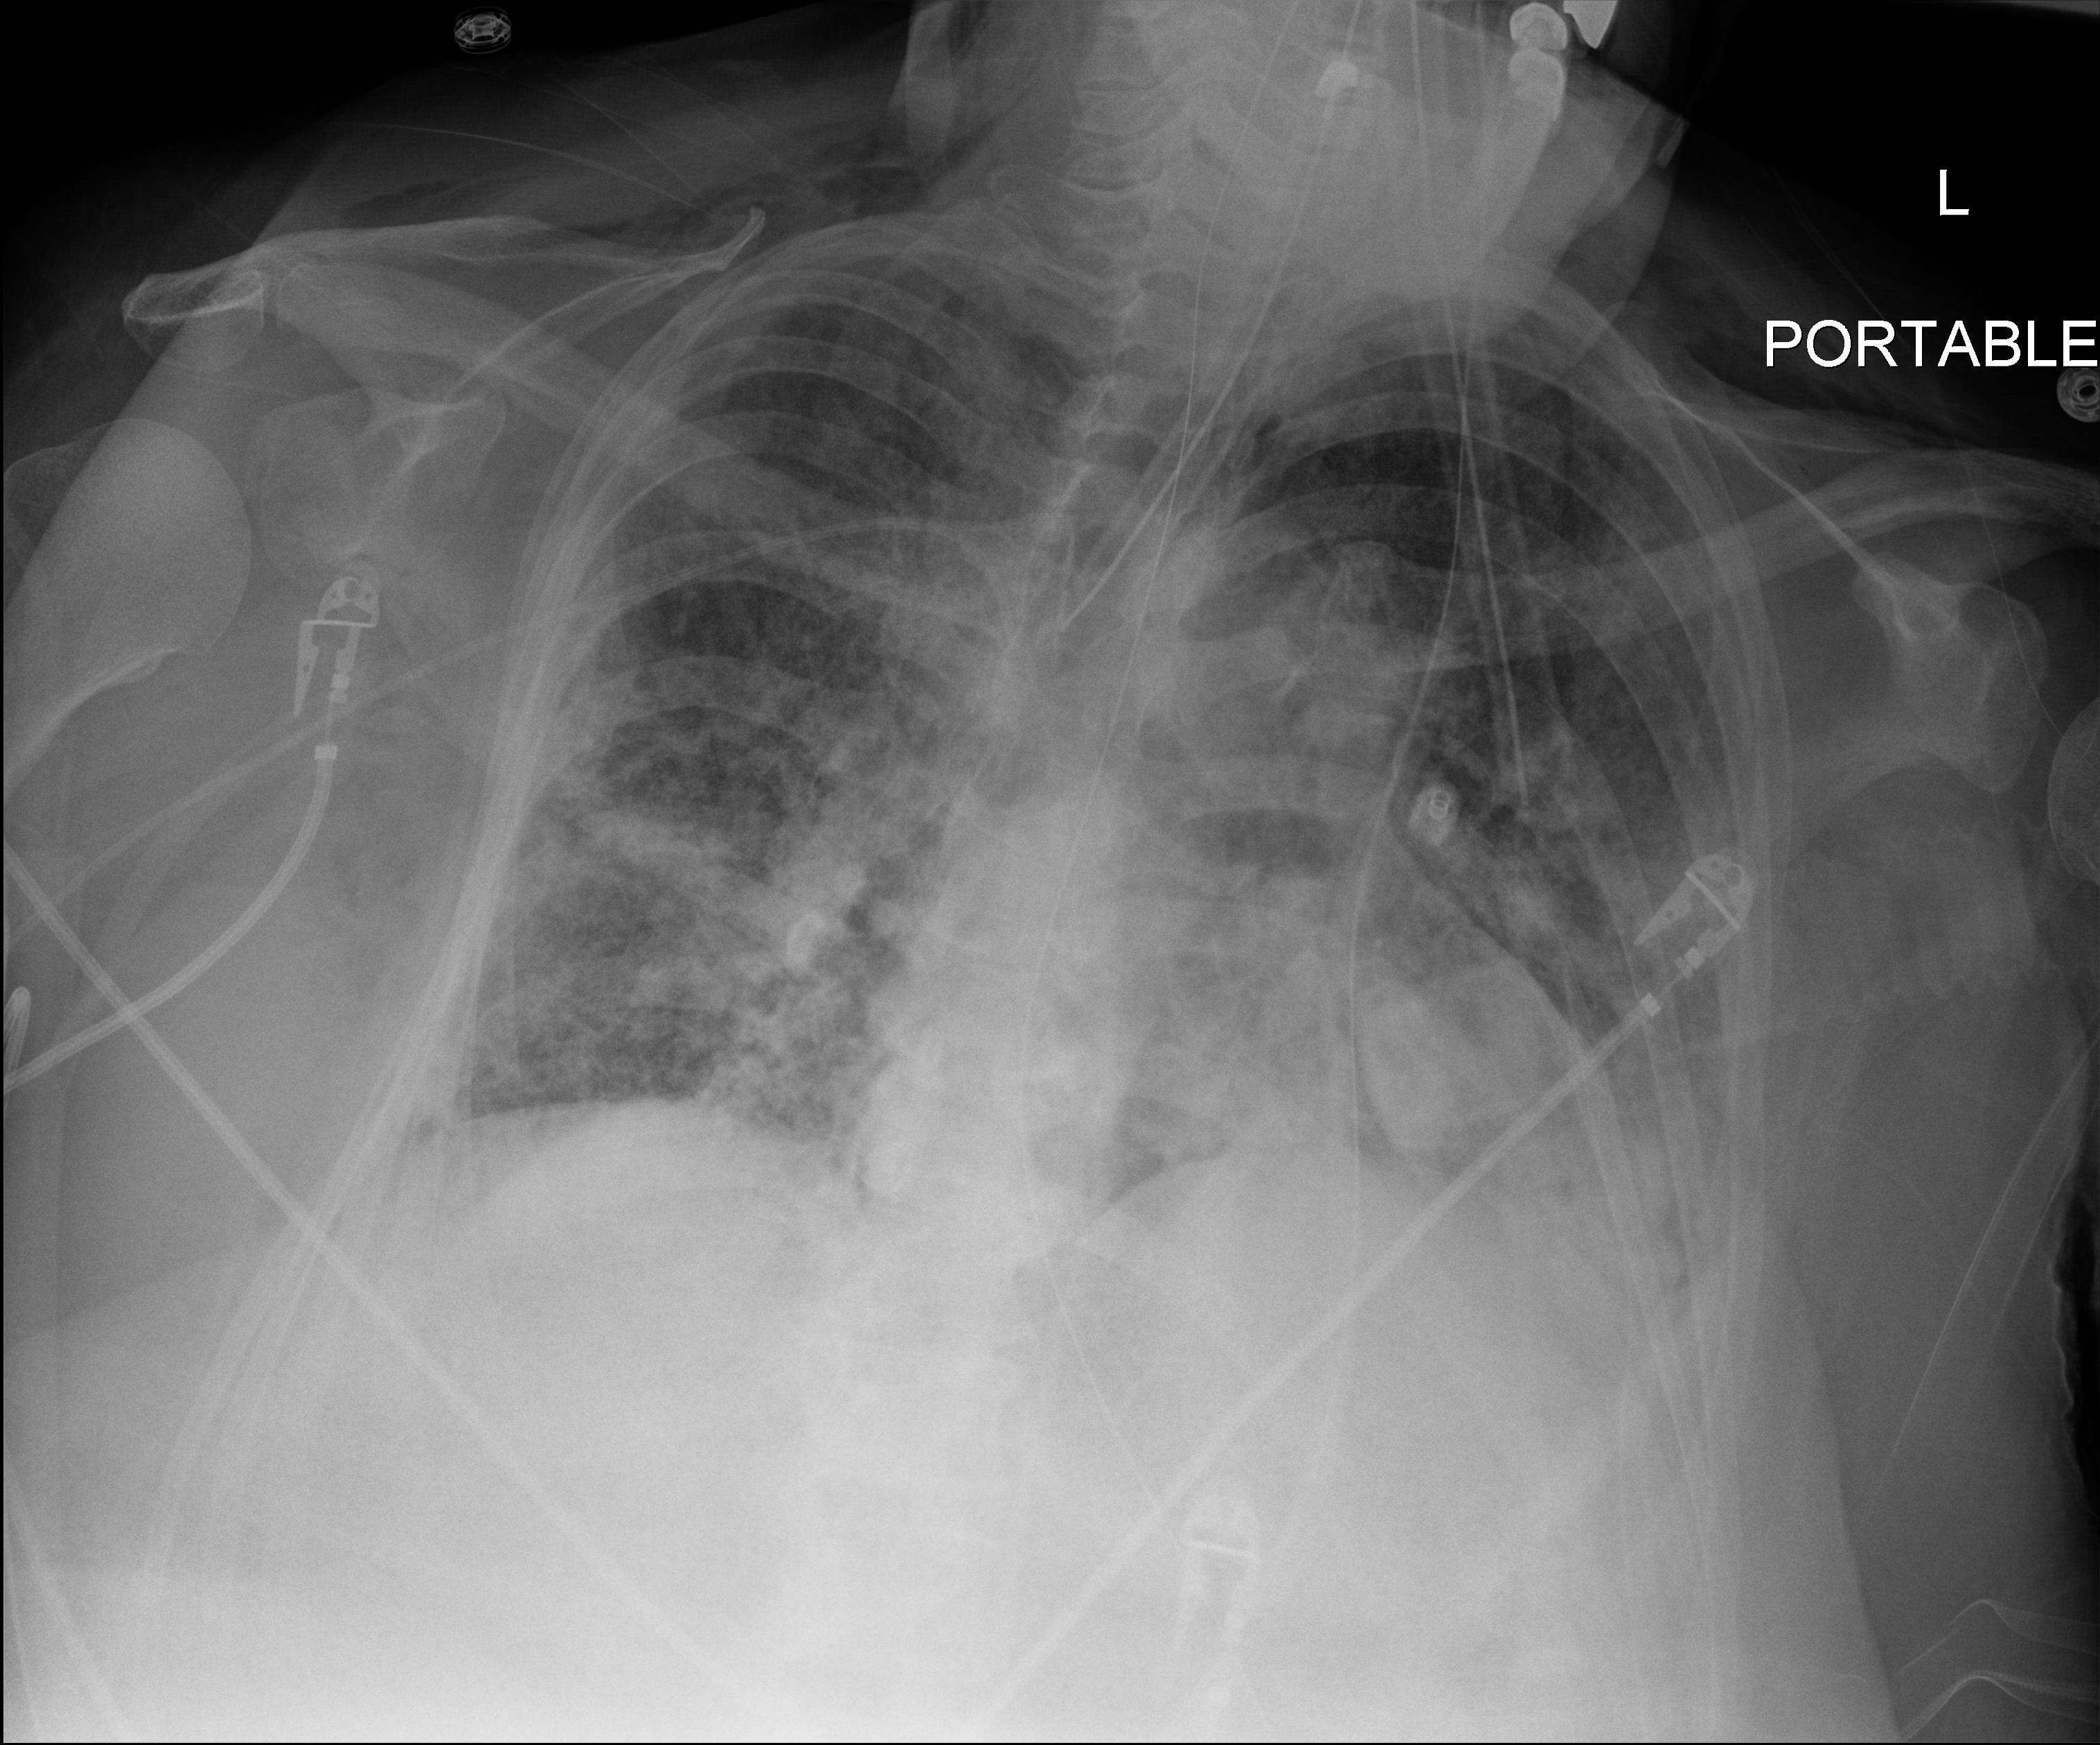
Bedside chest radiograph (digital radiography). Female patient hospitalised with COVID-19, age 60–74 years.
From the hospital-stay record, not from the radiograph (when in the stay this image was taken is not recorded):
- admitted to intensive care during this hospital stay: yes